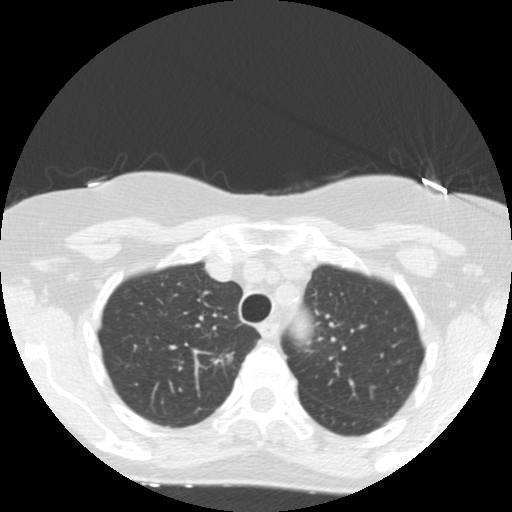
Low-dose screening chest CT, one axial slice; position 120 of 155 along the scan axis; 120 kVp; lung window (W 1500 / L -600 HU); 2.5 mm slice thickness; 512 × 512 image matrix.
Structures marked on this image (outlined manually by an expert reader):
- lesion 1 (tumor, upper lobe of right lung): bounding box <212,352,234,364> (left, top, right, bottom; pixels)